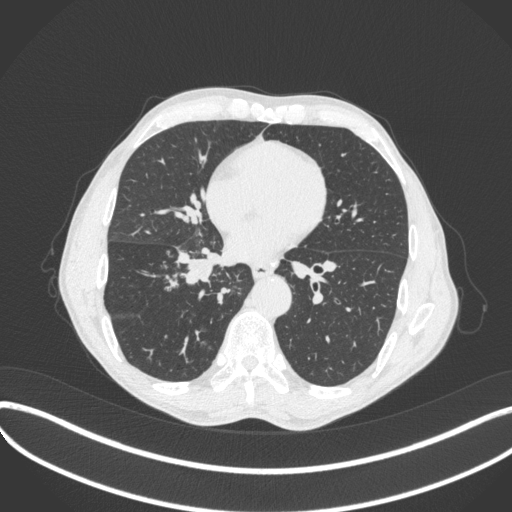
Chest CT, one axial slice; position 188 of 481 along the scan axis; reconstruction kernel B31f; lung window (W 1500 / L -600 HU); 1 mm slice thickness; 512 × 512 image matrix, field of view 400 × 400 mm. Patient: male, 65 years. Case-level facts recorded for this patient, not image findings: clinical TNM (as recorded): T2a N0 M0; histopathological grade: G2.
Annotated regions visible in this slice (rectangle marked by the reading radiologist):
- lung tumour (recorded histology: squamous cell carcinoma): bounding box [x1, y1, x2, y2] px = [176, 246, 226, 287]